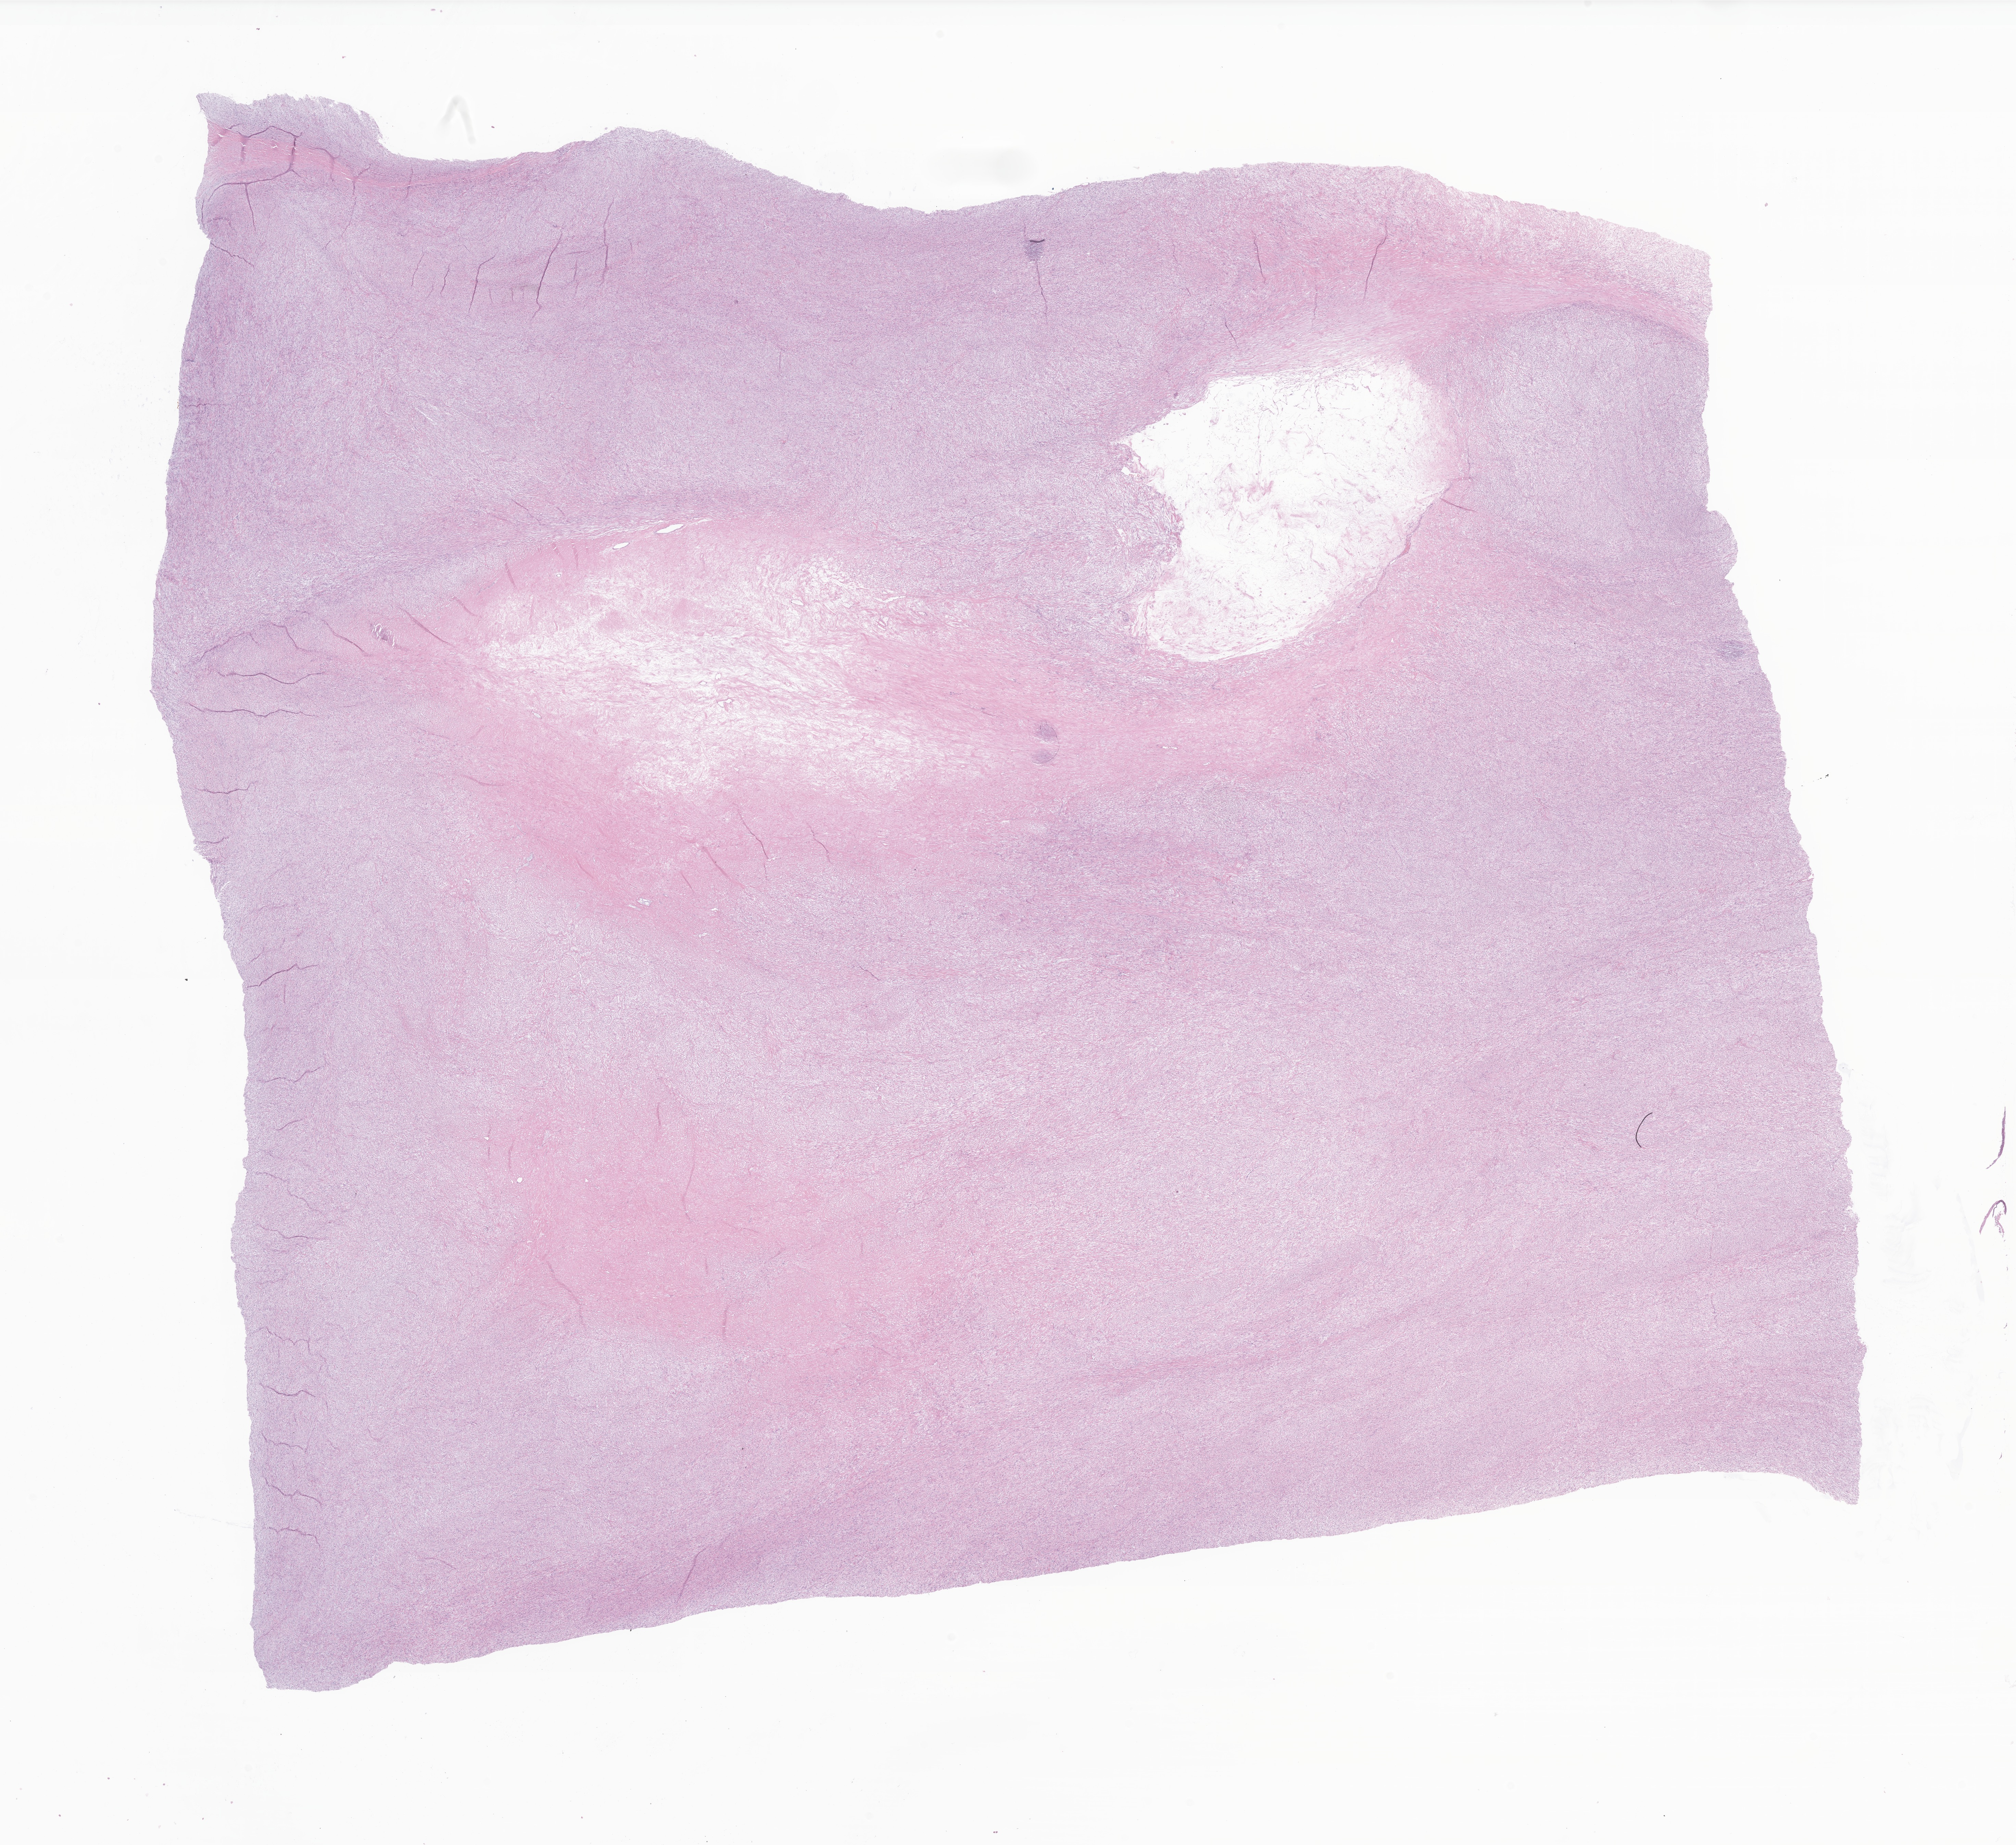
Whole-slide image, haematoxylin and eosin stain of tumor tissue from the abdomen, whole scanned area (about 24.8 x 22.7 mm) shown as a low-resolution overview; formalin-fixed, paraffin-embedded (FFPE) tissue. Patient: male, age 101 months (8 years 5 months).
* recorded diagnosis: Myofibroma